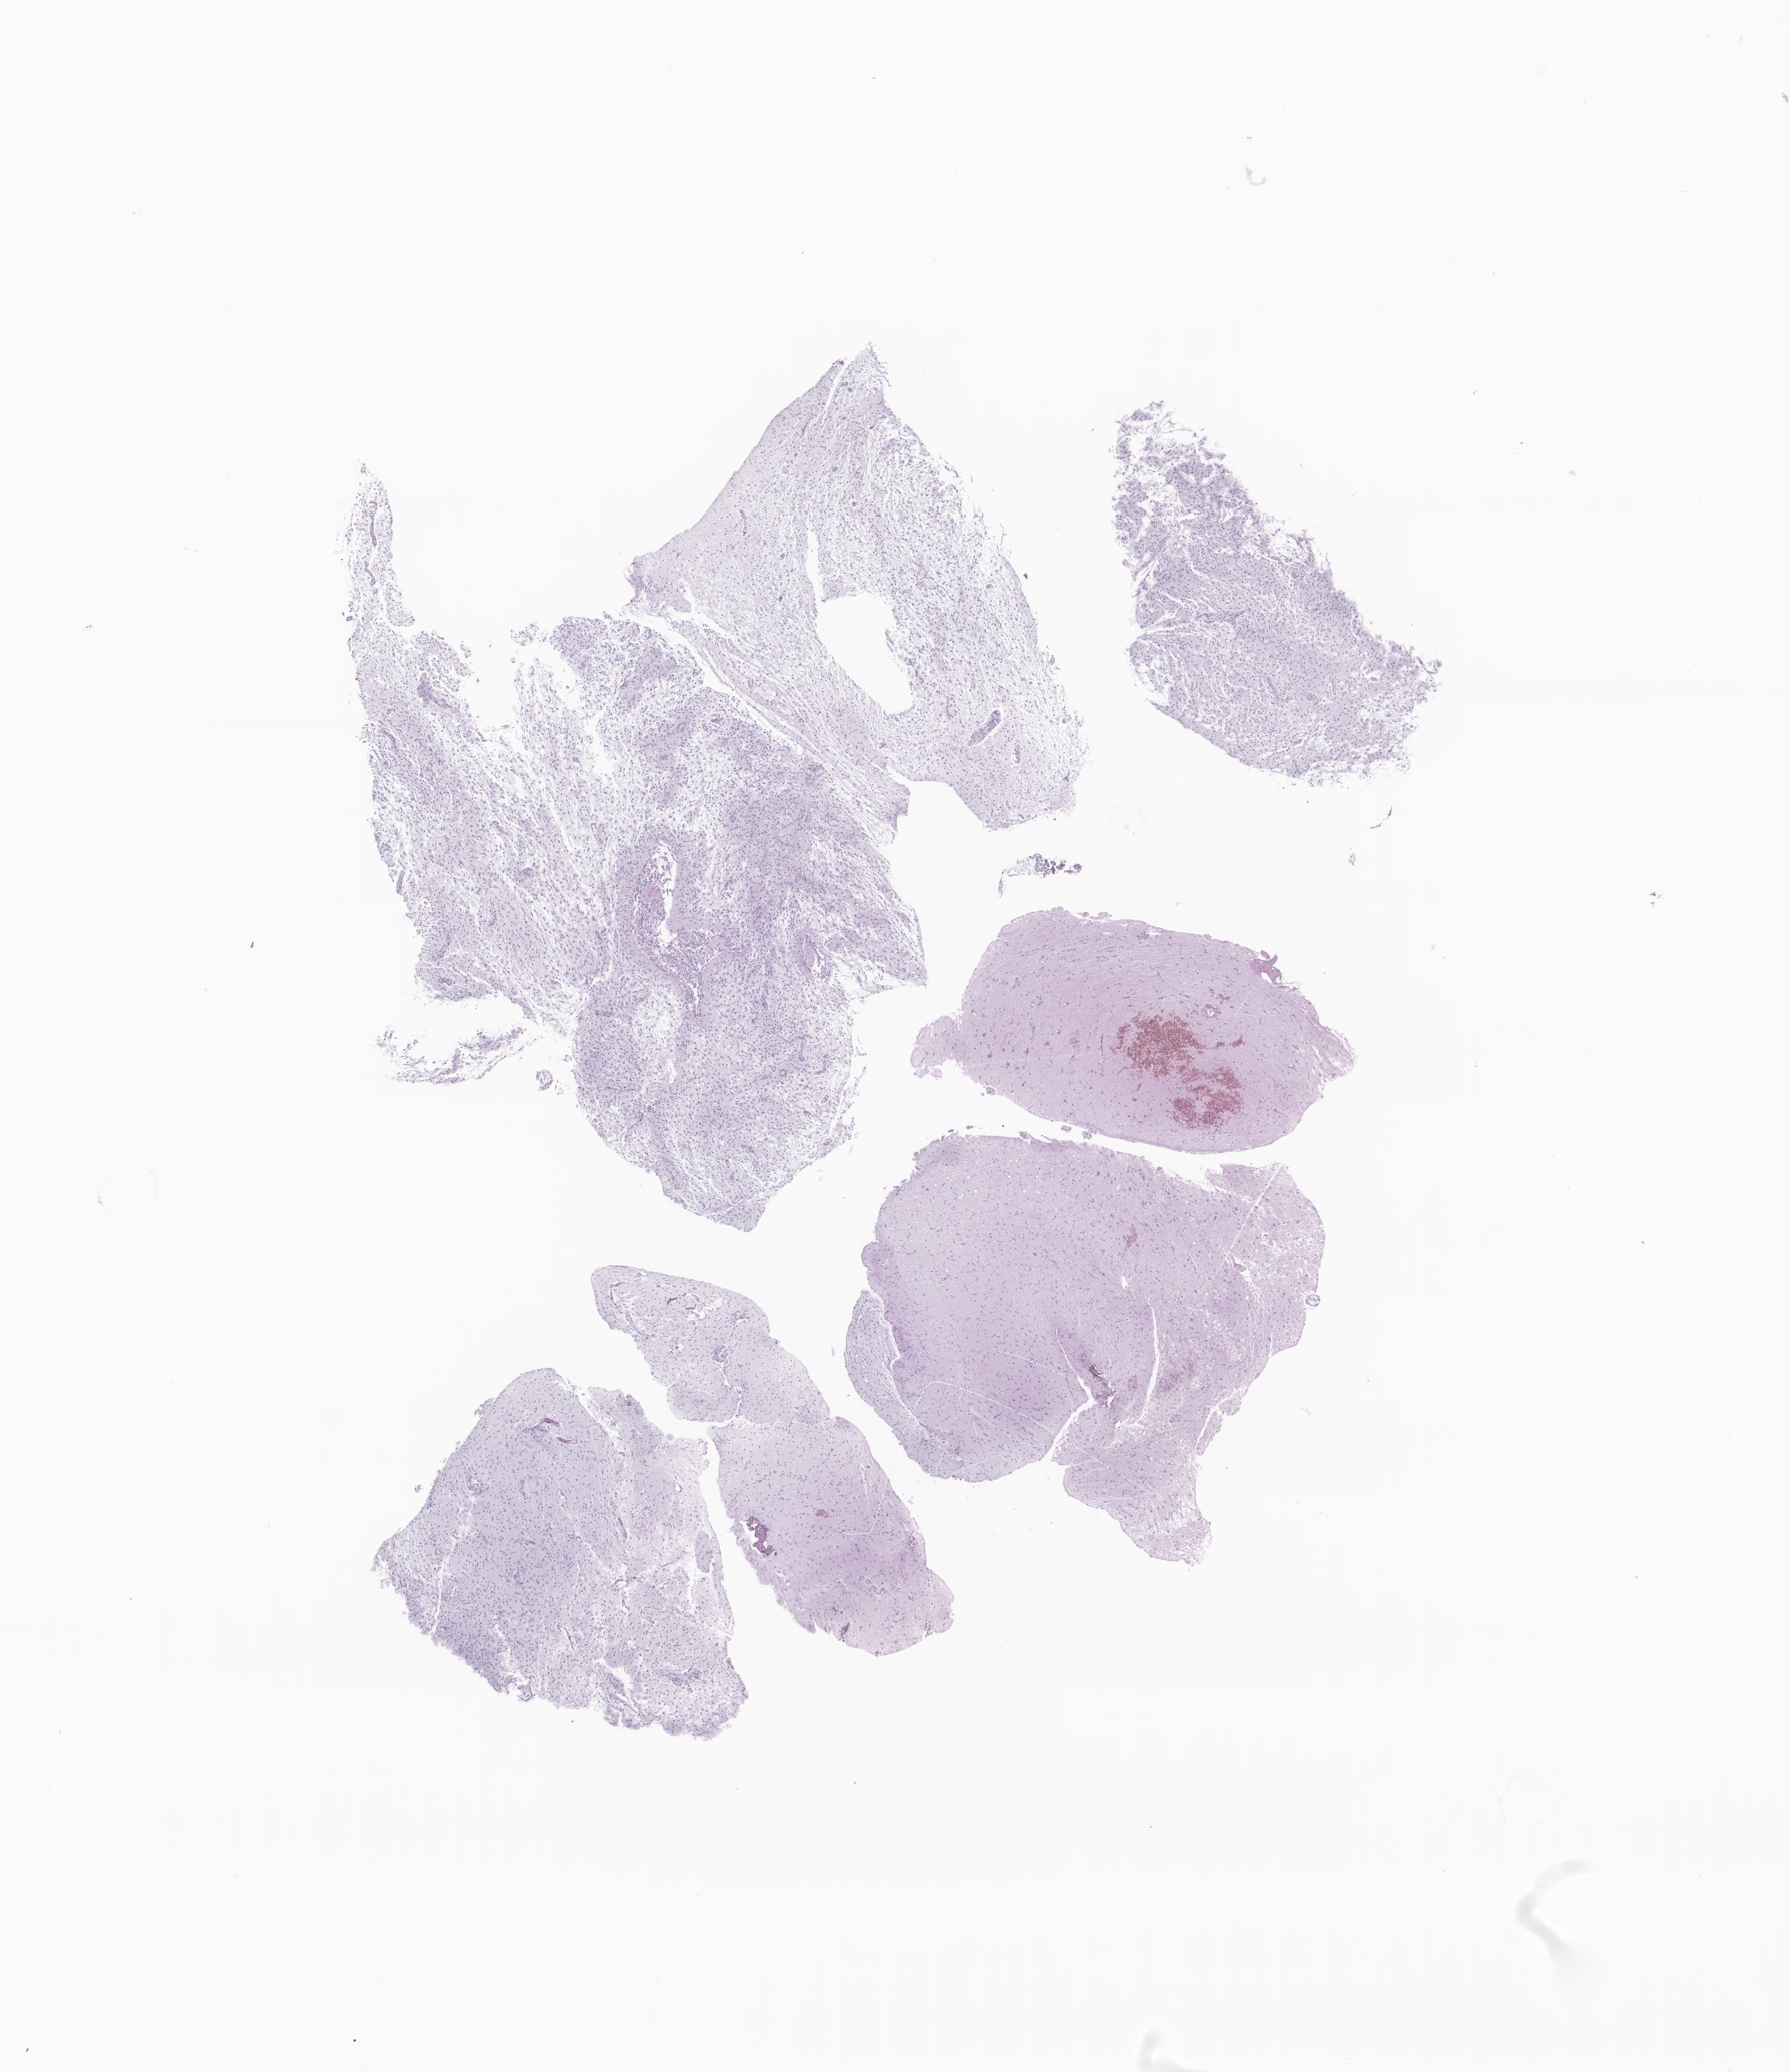
Whole-slide image, hematoxylin and eosin (H&E) stain of tumor tissue from the cerebrum — shown as a low-resolution overview of the whole scanned area (about 9.7 x 11.3 mm); formalin-fixed, paraffin-embedded (FFPE) tissue. Patient female; age 823 days (about 2.3 years).
* diagnosis: Tumor cells, uncertain whether benign or malignant